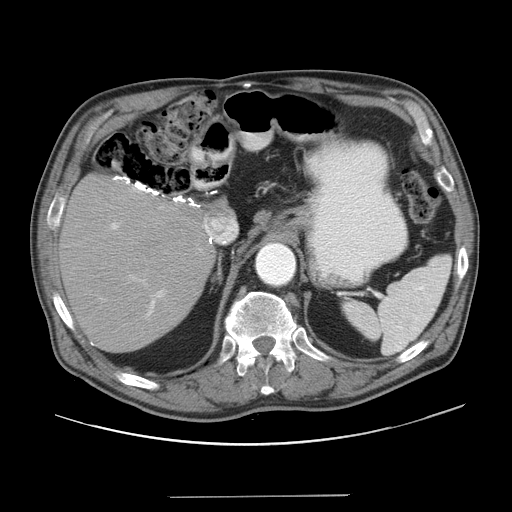
Contrast-enhanced abdominal CT, one axial slice; slice 29 of 41 in the series (ordered by position); reconstruction kernel STANDARD; intravenous contrast given; soft-tissue window (W 400 / L 40 HU); 5 mm slice thickness; 512 × 512 image matrix, field of view 420 × 420 mm. Male patient, age 75 years. From the clinical record (not read from this slice): diagnosis: colorectal cancer liver metastases, imaged before liver resection; multiple liver metastases: no; largest metastasis: 5.2 cm.
Annotated regions visible in this slice (manually delineated by an expert):
- hepatic veins: bounding box (x1, y1, x2, y2) in pixels: (204, 216, 236, 242)
- liver: (63, 179, 212, 352)
- planned liver remnant (the part of the liver to remain after resection): (63, 180, 213, 352)
- portal vein (with intrahepatic branches): (110, 206, 166, 318)